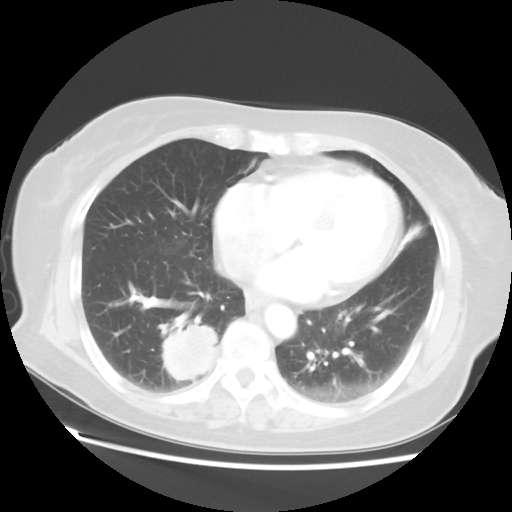
Chest CT, one axial slice. Reconstruction kernel STANDARD. 120 kVp. Lung window (W 1500 / L -600 HU). 5 mm slice thickness. 512 × 512 image matrix, field of view 356 × 356 mm. Patient: female, 69 years. Case-level facts recorded for this patient, not image findings: clinical TNM (as recorded): T2 N1 M1a.
Structures marked on this image (bounding box drawn by a radiologist):
- lung tumour (recorded histology: adenocarcinoma): bounding box (x1, y1, x2, y2) in pixels: (156, 313, 215, 386)